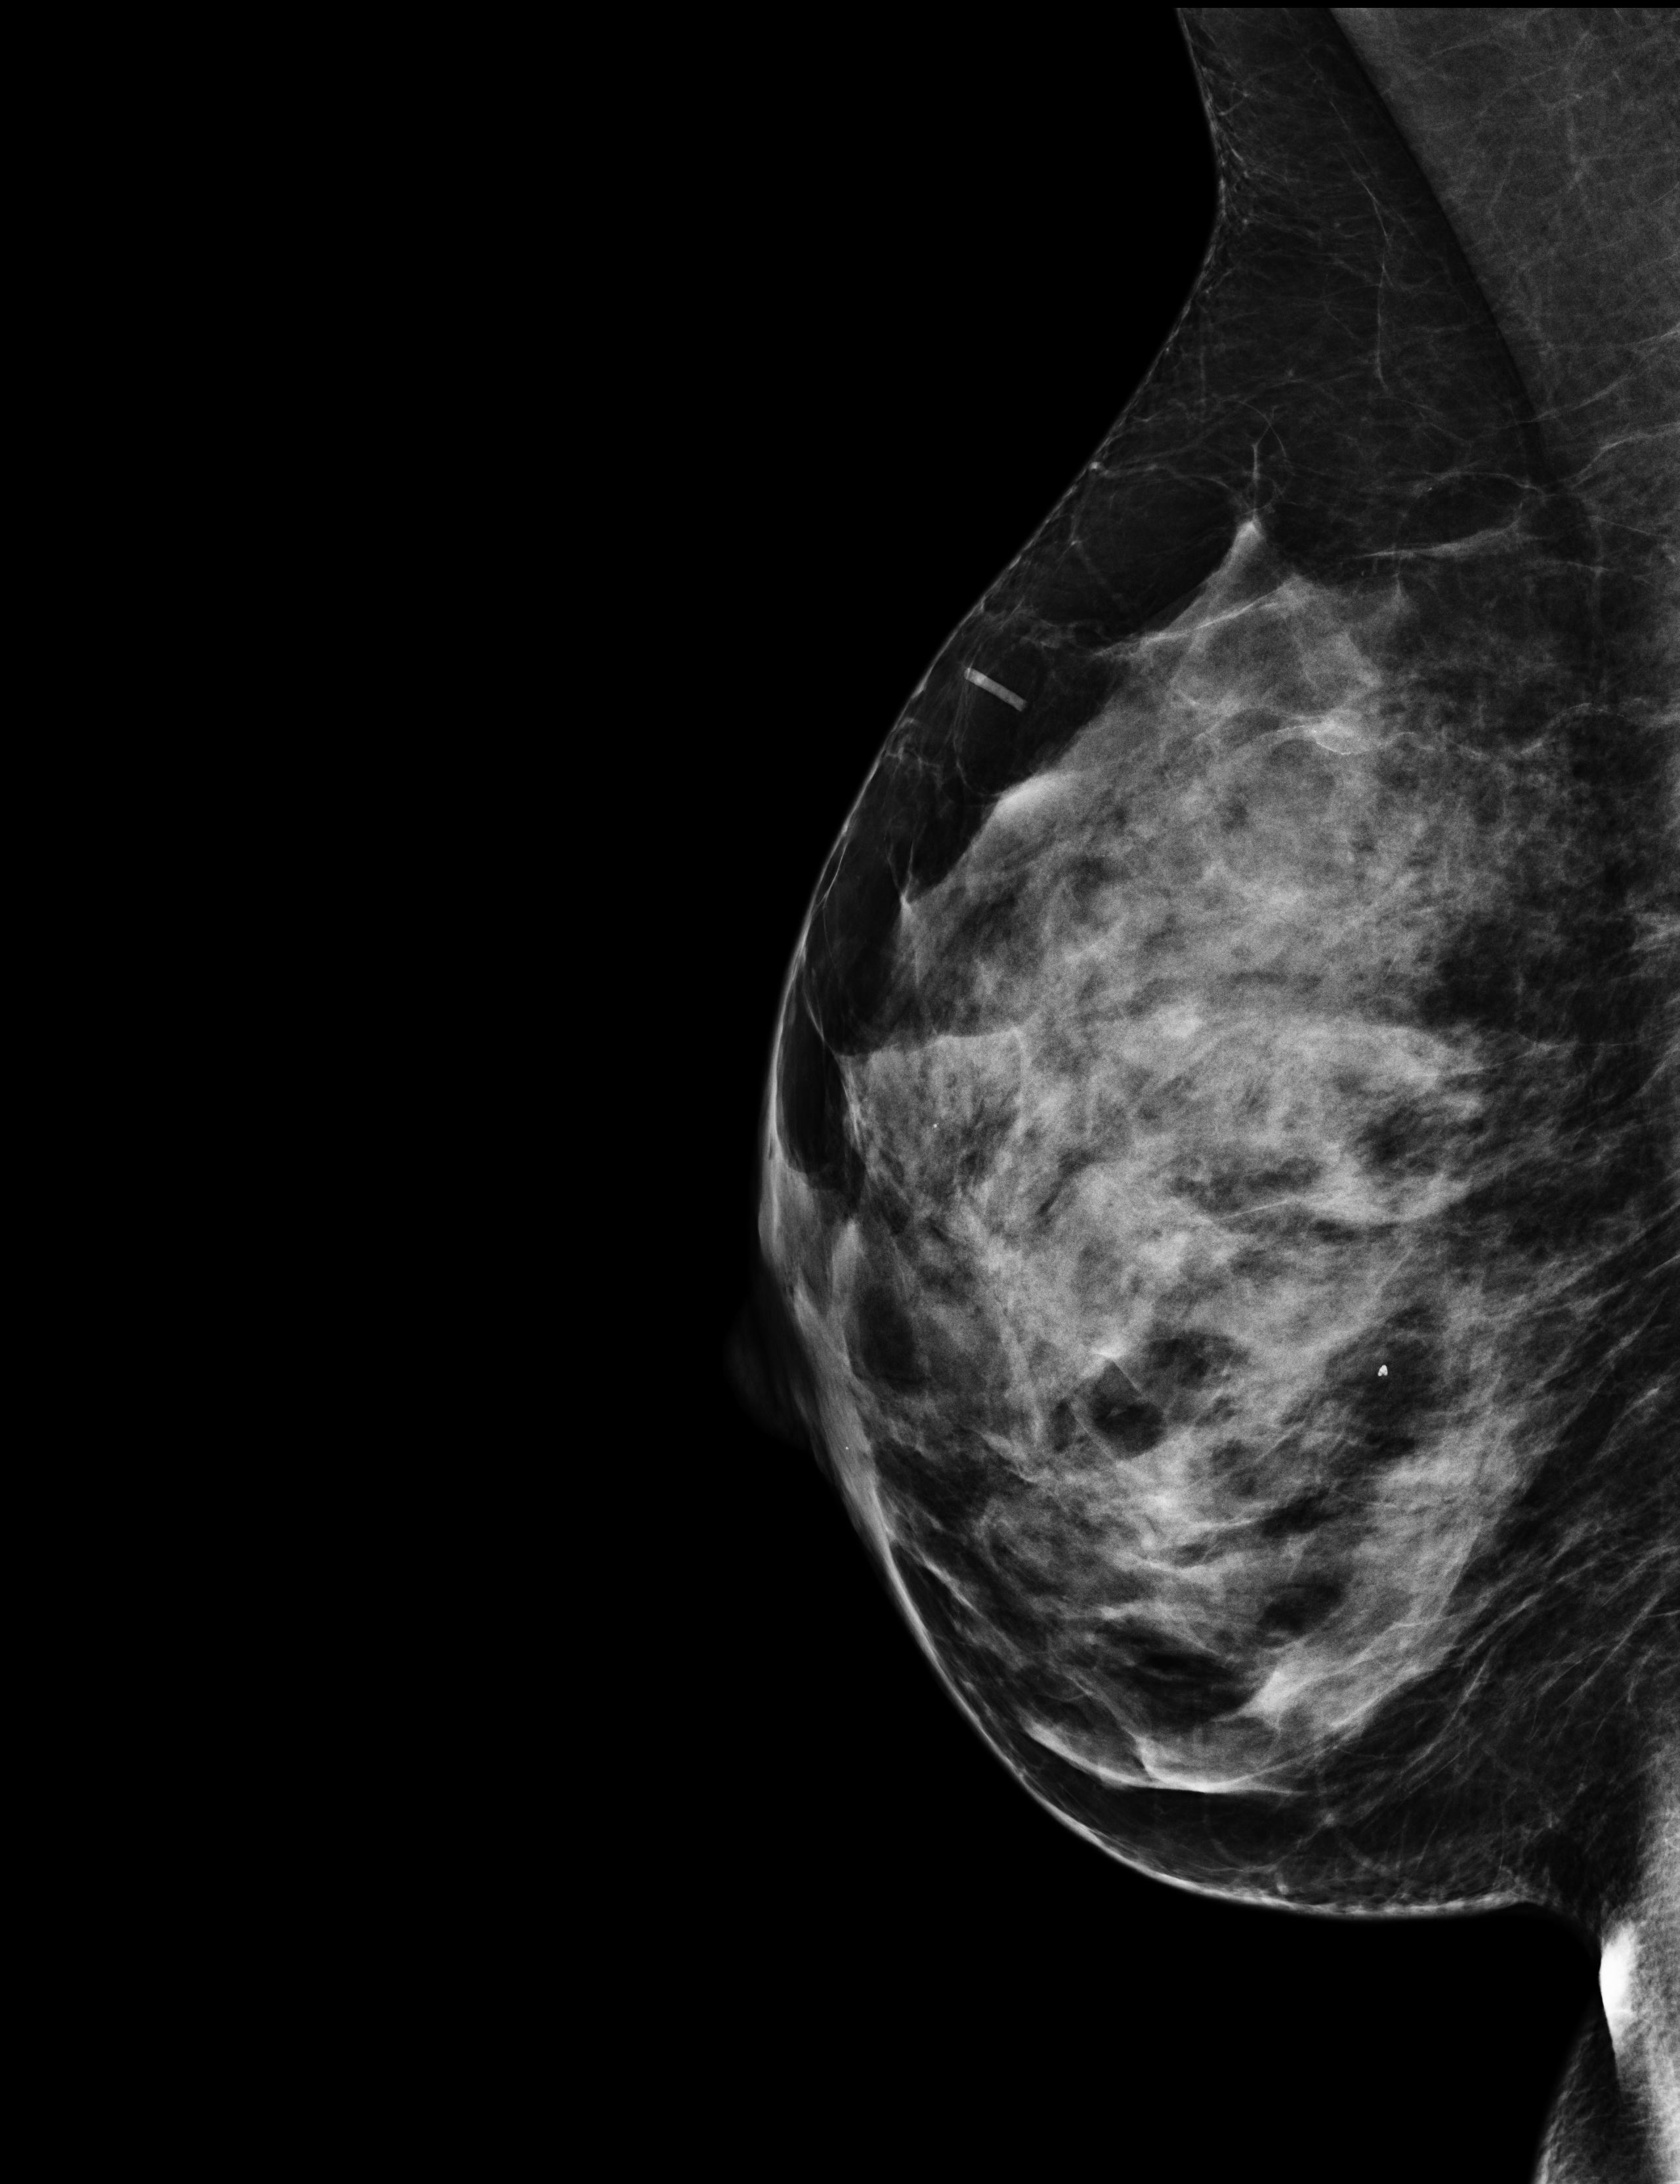
Digital mammogram (FFDM), right breast, MLO view, screening examination, compressed breast thickness 57 mm, system: Selenia Dimensions. Patient: female, 47 years.
Breast density at the screening exam (both breasts): heterogeneously dense (BI-RADS density category c). Final BI-RADS category for the screening round (tomosynthesis exam, both breasts): category 4. Recall: recalled for additional imaging after this screen.